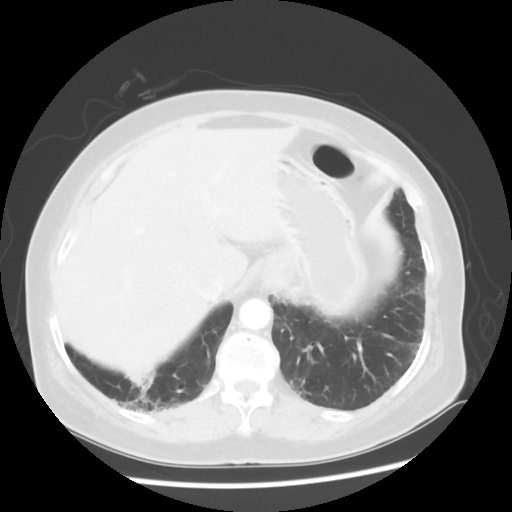
Chest CT, one axial slice; slice 11 of 56 in the series (ordered by position); reconstruction kernel STANDARD; 120 kVp; lung window (W 1500 / L -600 HU); 512 × 512 image matrix, field of view 360 × 360 mm. Patient: female, 64 years. From the clinical record (not read from this slice): clinical TNM (as recorded): Tis N0 M0.
Annotated regions visible in this slice (bounding box drawn by a radiologist):
- lung tumour (recorded histology: adenocarcinoma): box from (x=122, y=369) to (x=166, y=424) px